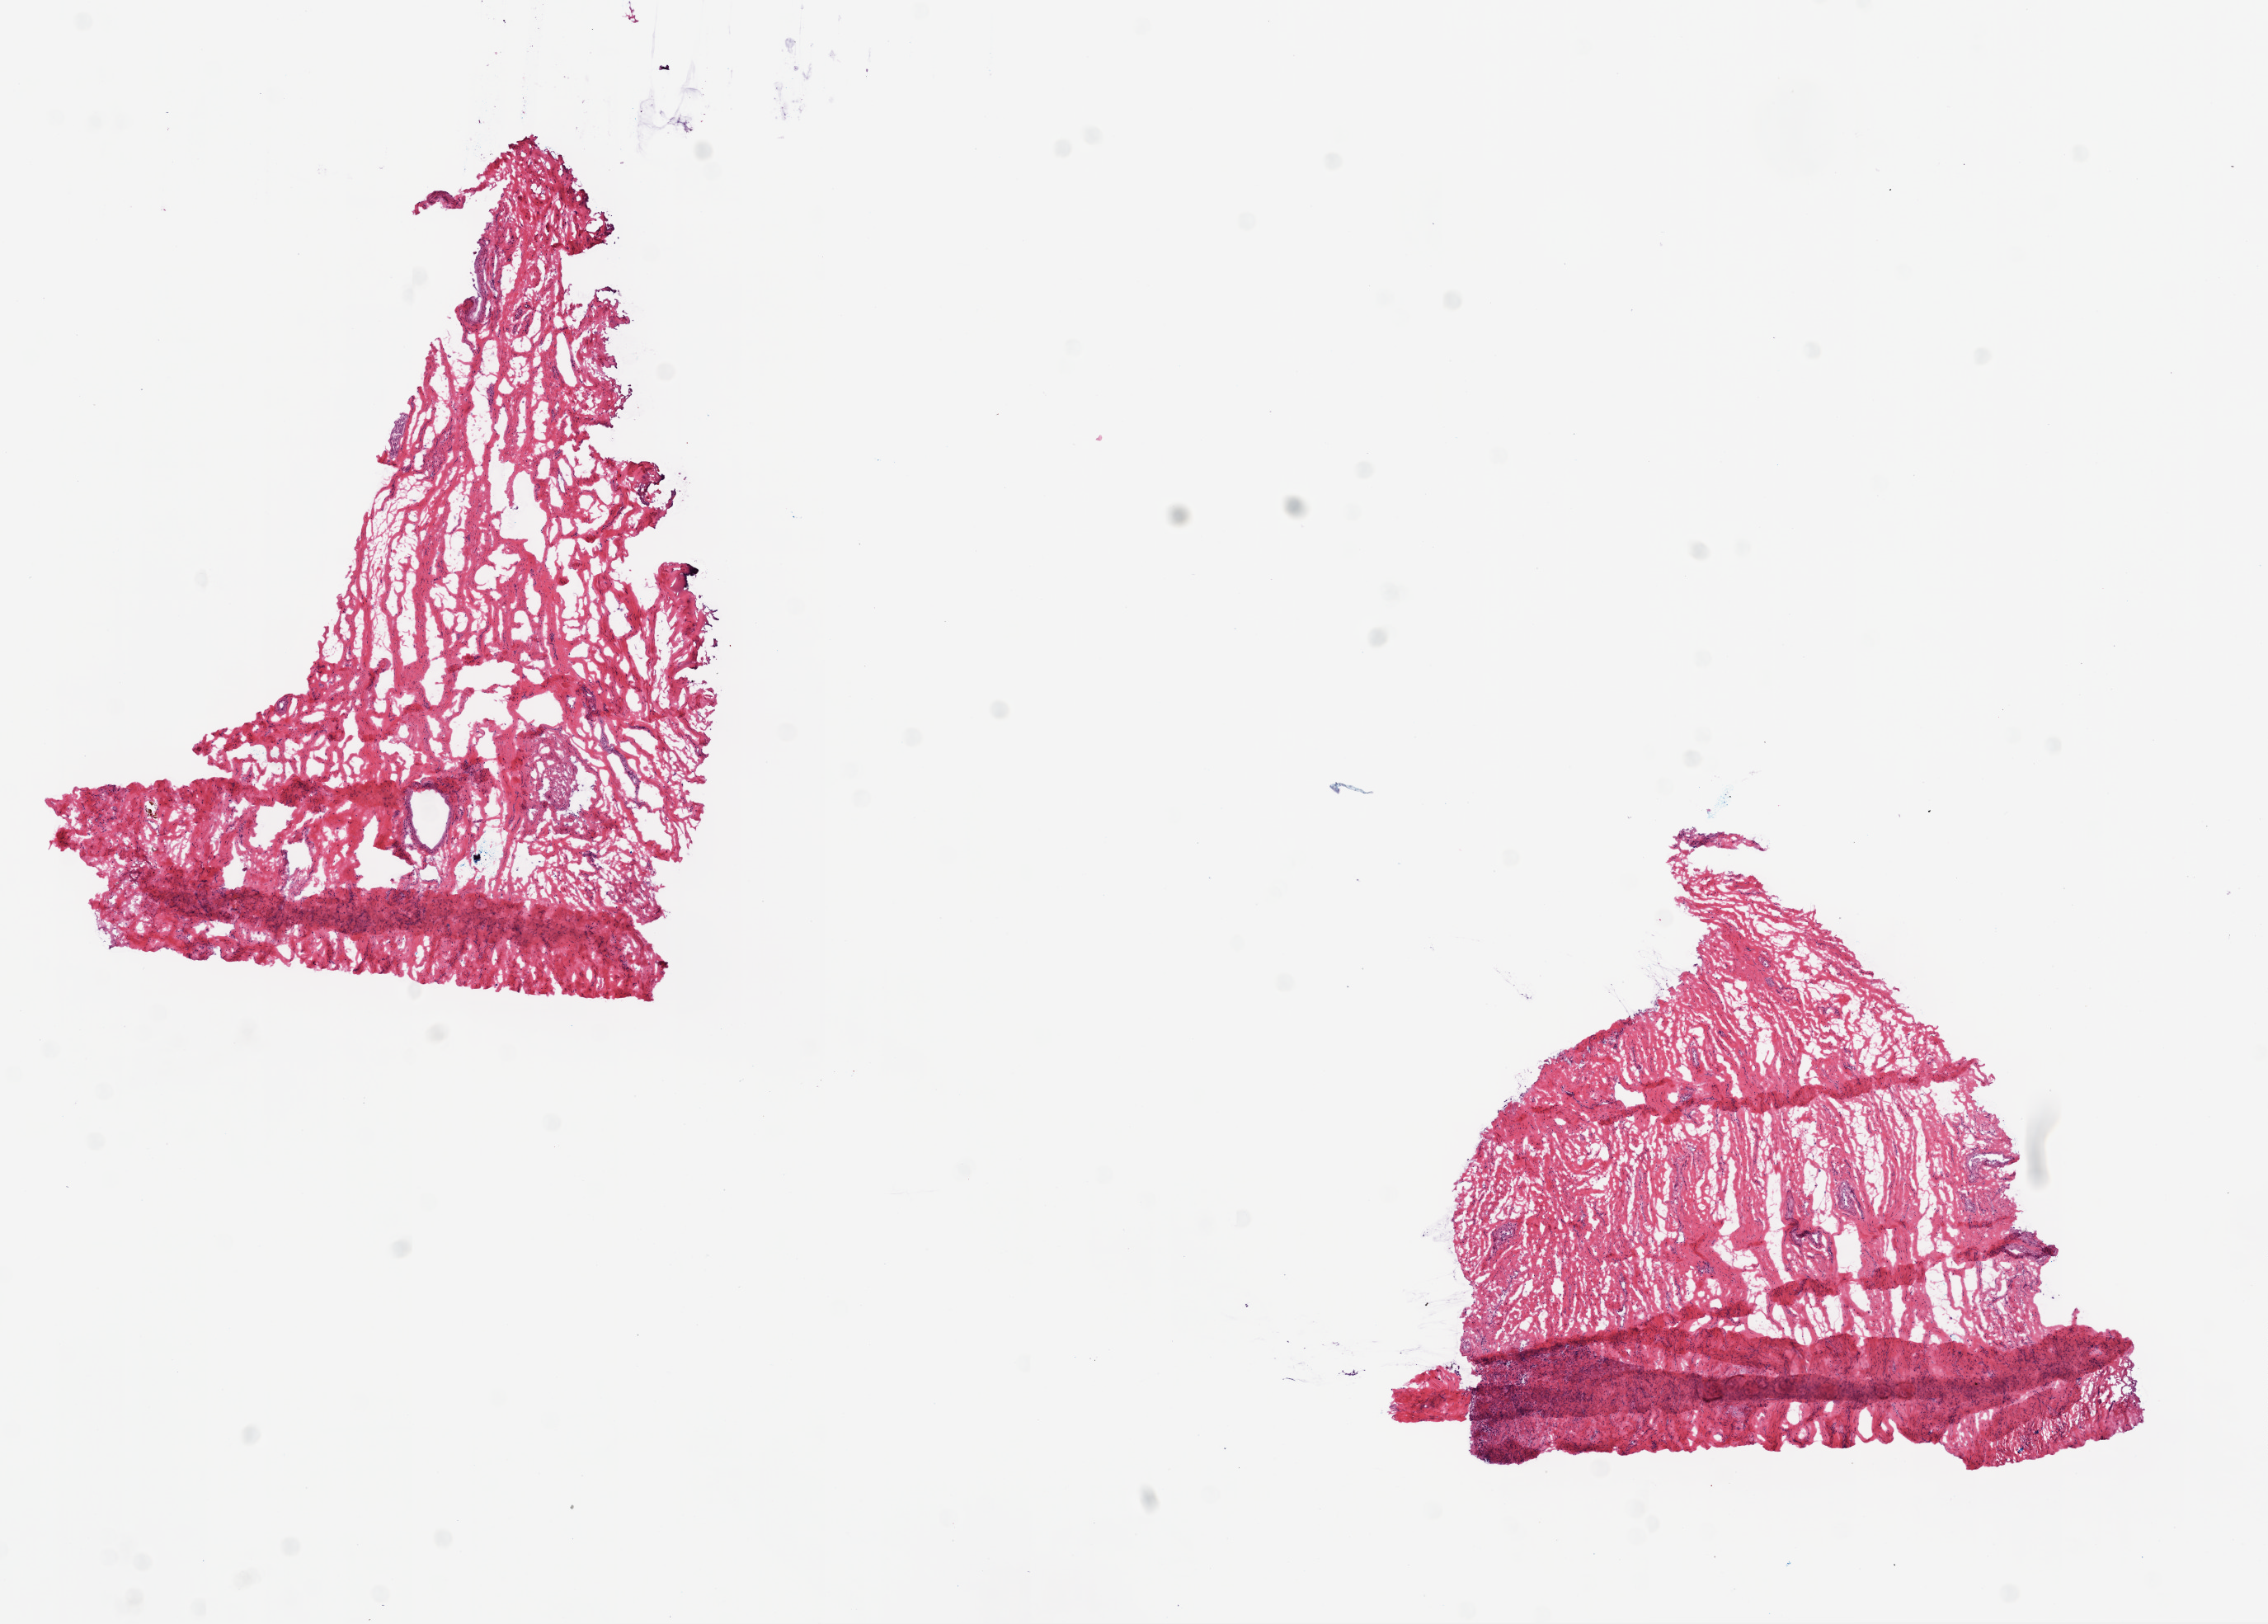
H&E-stained whole-slide image, low-resolution overview of the scanned area, about 11.0 x 7.9 mm (slide scanned at 20x); frozen section from the bottom of the tissue portion; sample: solid tissue normal (non-tumour tissue), ovary. Female, age 48 years at initial diagnosis.
* this section: solid tissue normal sample (biorepository sample class)
* patient diagnosis: Serous cystadenocarcinoma, NOS